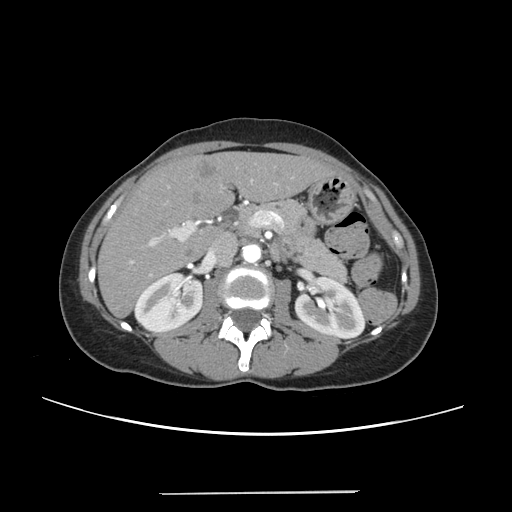
Contrast-enhanced abdominal CT, one axial slice; position 124 of 240 along the scan axis; 120 kVp; intravenous contrast given; soft-tissue window (W 400 / L 40 HU); 1.25 mm slice thickness; 512 × 512 image matrix, field of view 371 × 371 mm. Female patient, age 60 years. From the clinical record (not read from this slice): diagnosis: colorectal cancer liver metastases, imaged before liver resection.
Annotated regions visible in this slice (outlined manually by an expert reader):
- liver: bounding box [x1, y1, x2, y2] px = [100, 153, 330, 315]
- planned liver remnant (the part of the liver to remain after resection): [100, 154, 330, 315]
- portal vein (with intrahepatic branches): [130, 179, 278, 276]
- liver metastasis: [199, 161, 218, 179]